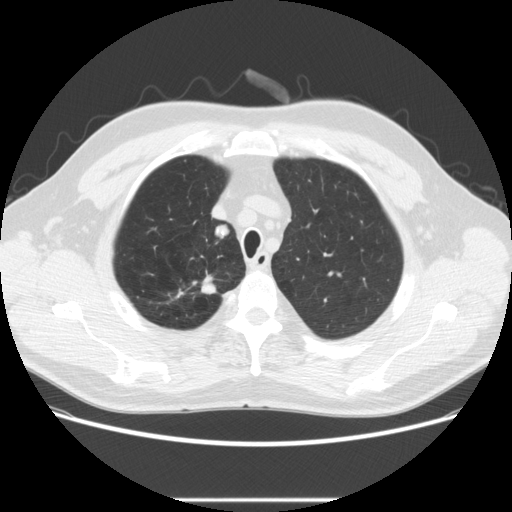
Low-dose screening chest CT, axial slice; baseline annual screen; lung window (W 1500 / L -600 HU); 2.5 mm slice thickness; slice 43 of 270 in the series; 512 × 512 image matrix, field of view 380 × 380 mm. Male, age 64 years at enrolment.
- 2 expert-annotated lung lesions on this slice (largest first), bounding box [x1, y1, x2, y2] px = [170, 275, 225, 305]; [207, 220, 236, 246].
- The screening reader recorded 2 non-calcified nodules or masses ≥4 mm on this exam (right upper lobe, right upper lobe); which of them these boxes mark is not recorded.
- Later outcome: lung cancer diagnosed 753 days after this screen — adenocarcinoma, NOS, right upper lobe, moderately differentiated (G2), stage IA (AJCC 6th edition), 14 mm at pathology.